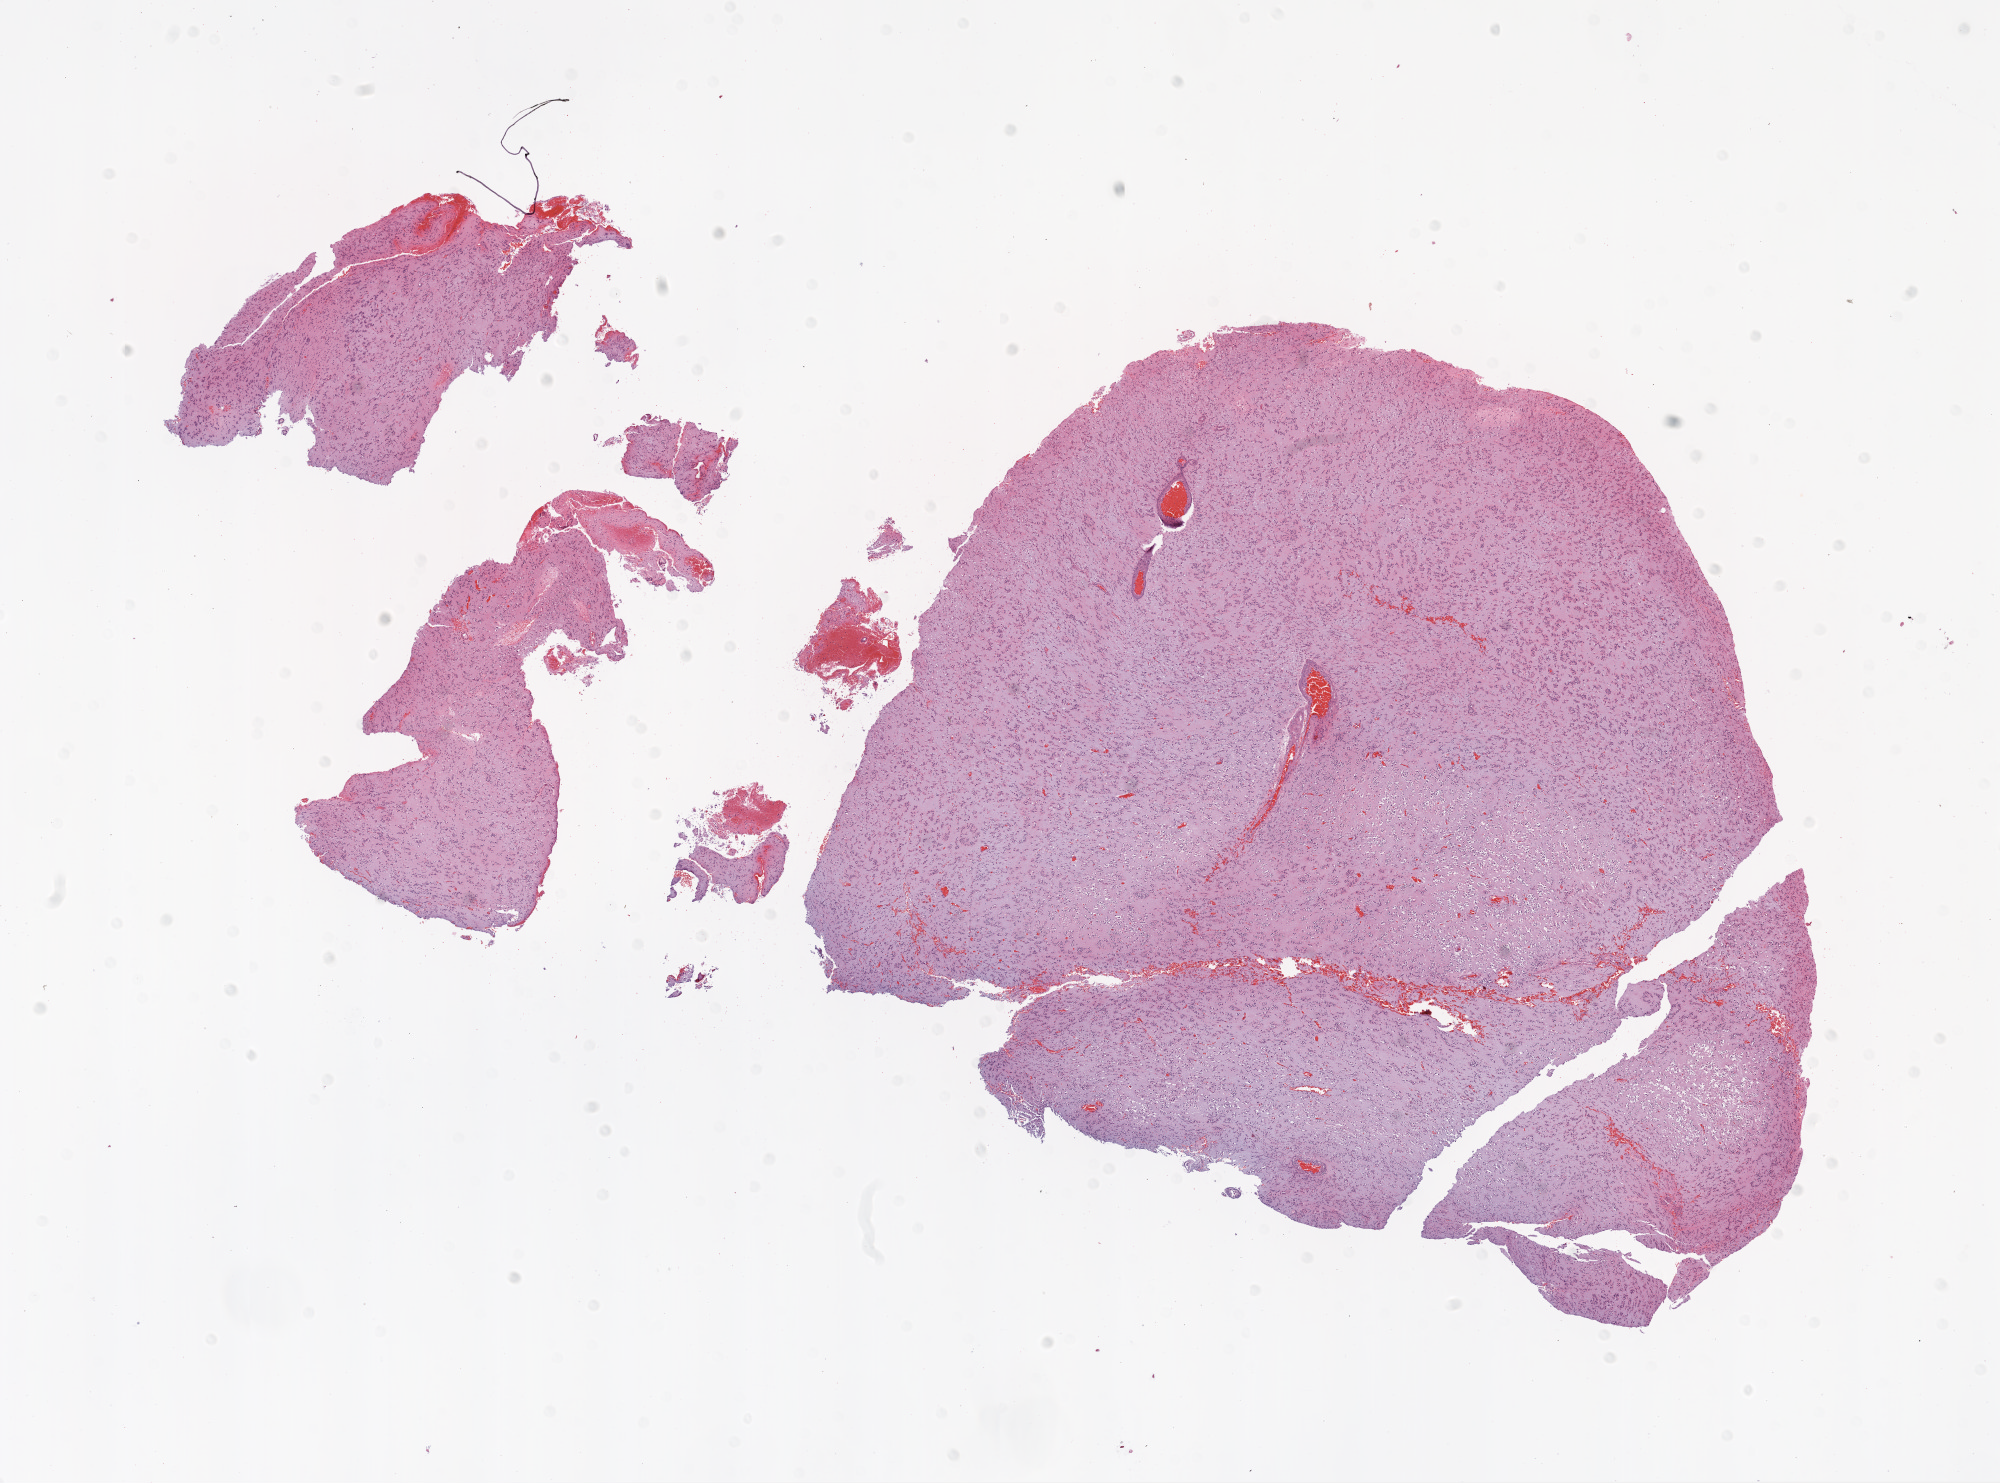
H&E whole-slide image, a low-resolution overview of the entire scanned area, about 16.0 x 11.9 mm (slide scanned at 20x), formalin-fixed paraffin-embedded (FFPE) diagnostic section, primary tumour sample from the brain. Male, age 71 years at initial diagnosis.
Pathologic diagnosis: Glioblastoma.